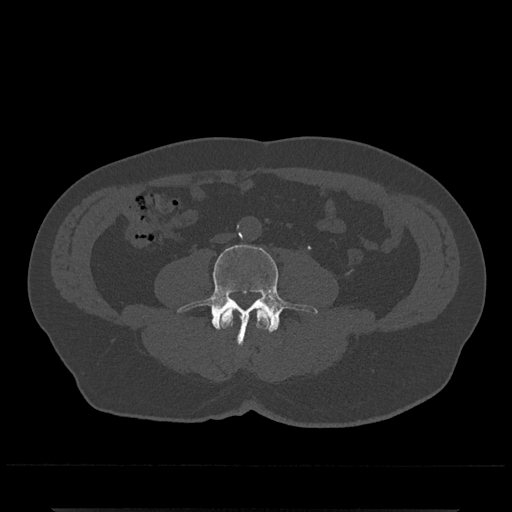
CT including the spine, one axial slice; position 167 of 797 along the scan axis; 120 kVp; bone window (W 1800 / L 400 HU); 0.5 mm slice thickness; 512 × 512 image matrix, field of view 393 × 393 mm. Male patient, age 67 years. Case-level facts recorded for this patient, not image findings: primary cancer: prostate.
Outlined on this slice (semi-automatically segmented with operator editing):
- L3 vertebra: bounding box [x1, y1, x2, y2] px = [219, 307, 271, 332]
- L4 vertebra: [178, 244, 318, 345]